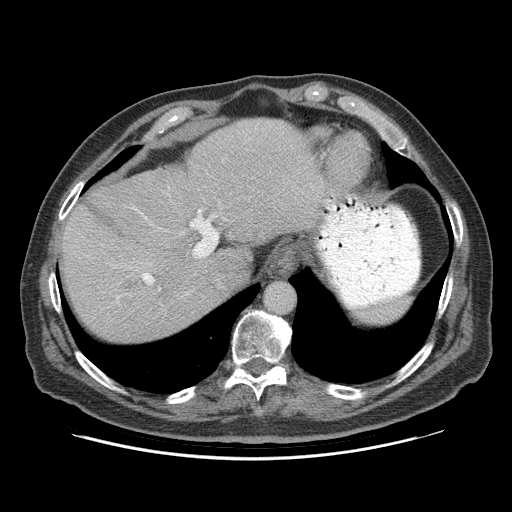
Contrast-enhanced abdominal CT (liver protocol), one axial slice. Slice 72 of 95 in the series (ordered by position). Reconstruction kernel STANDARD. Soft-tissue window (W 400 / L 40 HU). 2.5 mm slice thickness. 512 × 512 image matrix, field of view 400 × 400 mm. Case-level facts recorded for this patient, not image findings: diagnosis: hepatocellular carcinoma (patient treated with transarterial chemoembolisation; whether this scan precedes or follows treatment is not stated here); TNM stage (as recorded): Stage-IVB; Child-Pugh class: A; tumour differentiation: well differentiated.
Outlined on this slice (semi-automatic segmentation, software-assisted and operator-edited):
- abdominal aorta: box from (x=266, y=282) to (x=293, y=312) px
- liver parenchyma outside the tumour (the mass and vessels are separate outlines, so this box may not span the whole liver): (x=60, y=118)–(x=325, y=341)
- mass: (x=113, y=279)–(x=139, y=294)
- liver vessels: (x=142, y=210)–(x=210, y=284)